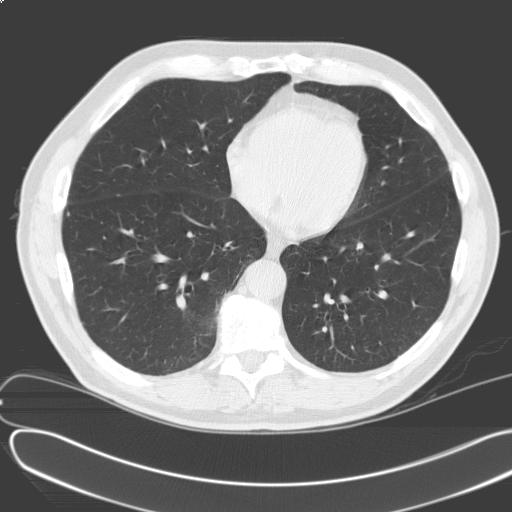
Axial slice from a low-dose chest CT screening exam. First (baseline) screen. Lung window (W 1500 / L -600 HU). 3.2 mm slice thickness. Standard (soft-tissue) reconstruction kernel (C). Male, age 69 years at enrolment.
Expert reader's lesion annotation, bounding box (x1, y1, x2, y2) in pixels: (218, 118, 247, 146). The screening reader recorded 2 non-calcified nodules or masses ≥4 mm on this exam (left upper lobe, right lower lobe); which of them this box marks is not recorded.